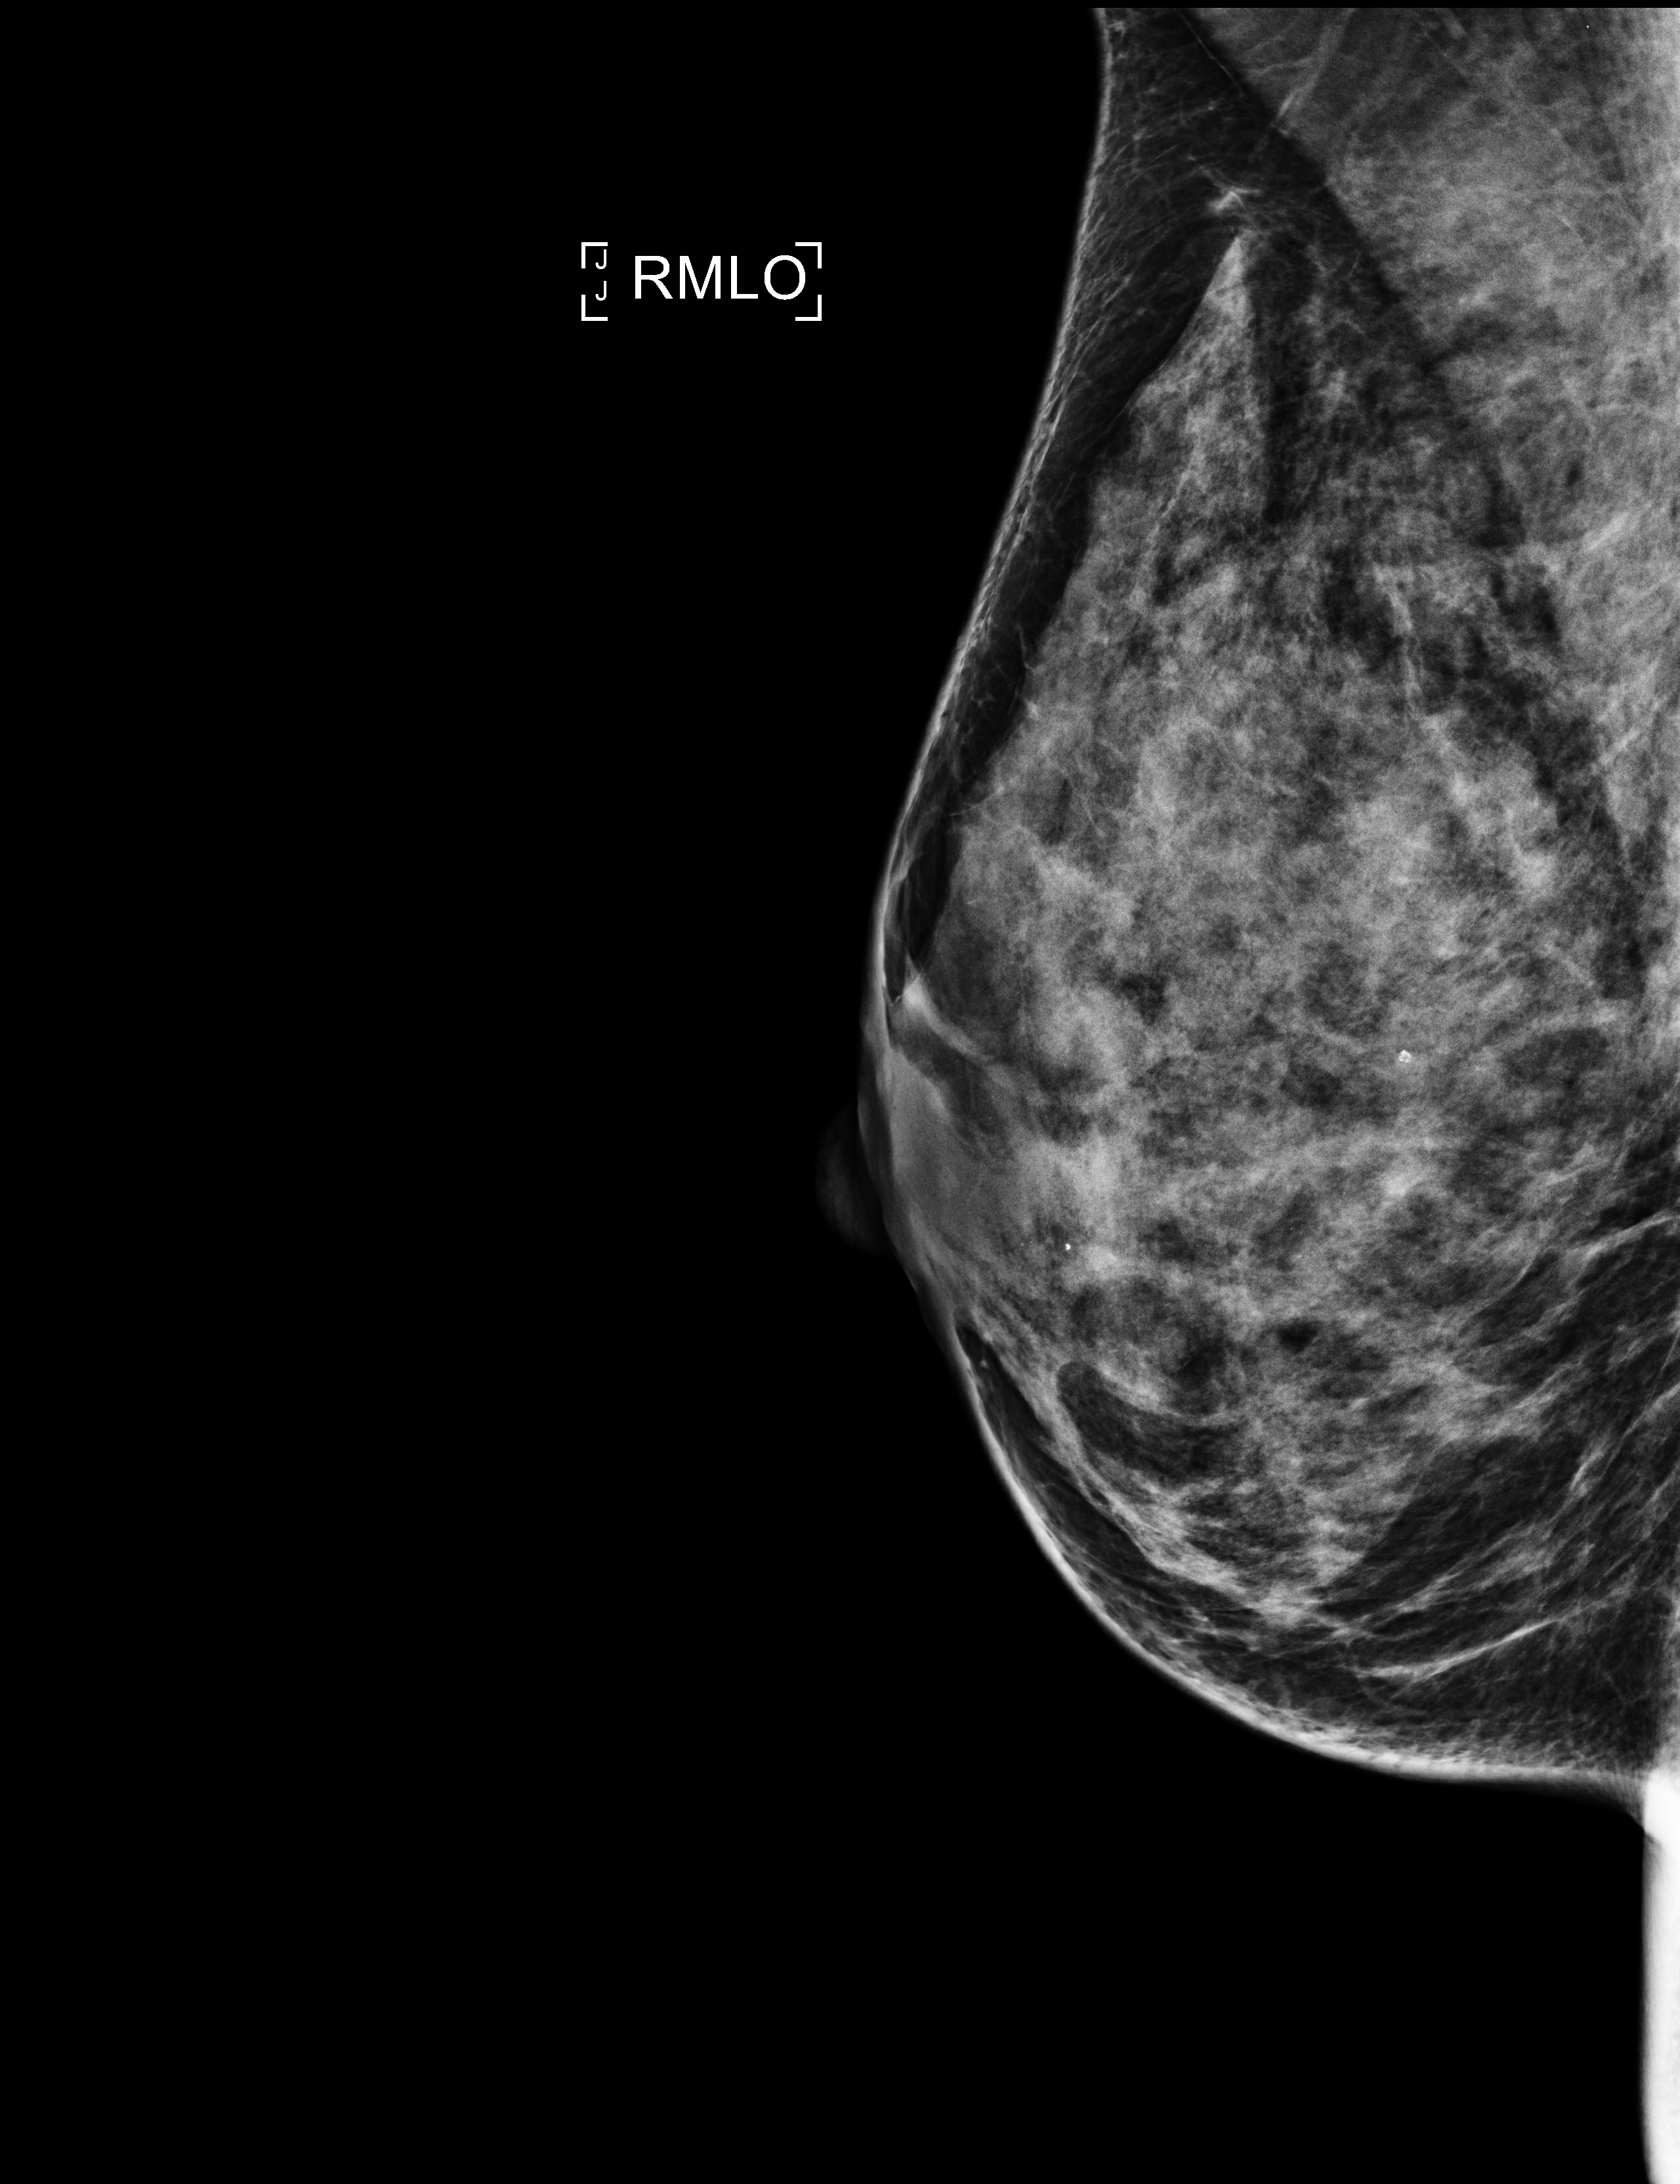
Screening examination, compressed breast thickness 55 mm, system: Selenia Dimensions. Patient aged 43 years (female).
Image type: full-field digital mammogram. Breast: right. Projection: medio-lateral oblique projection.